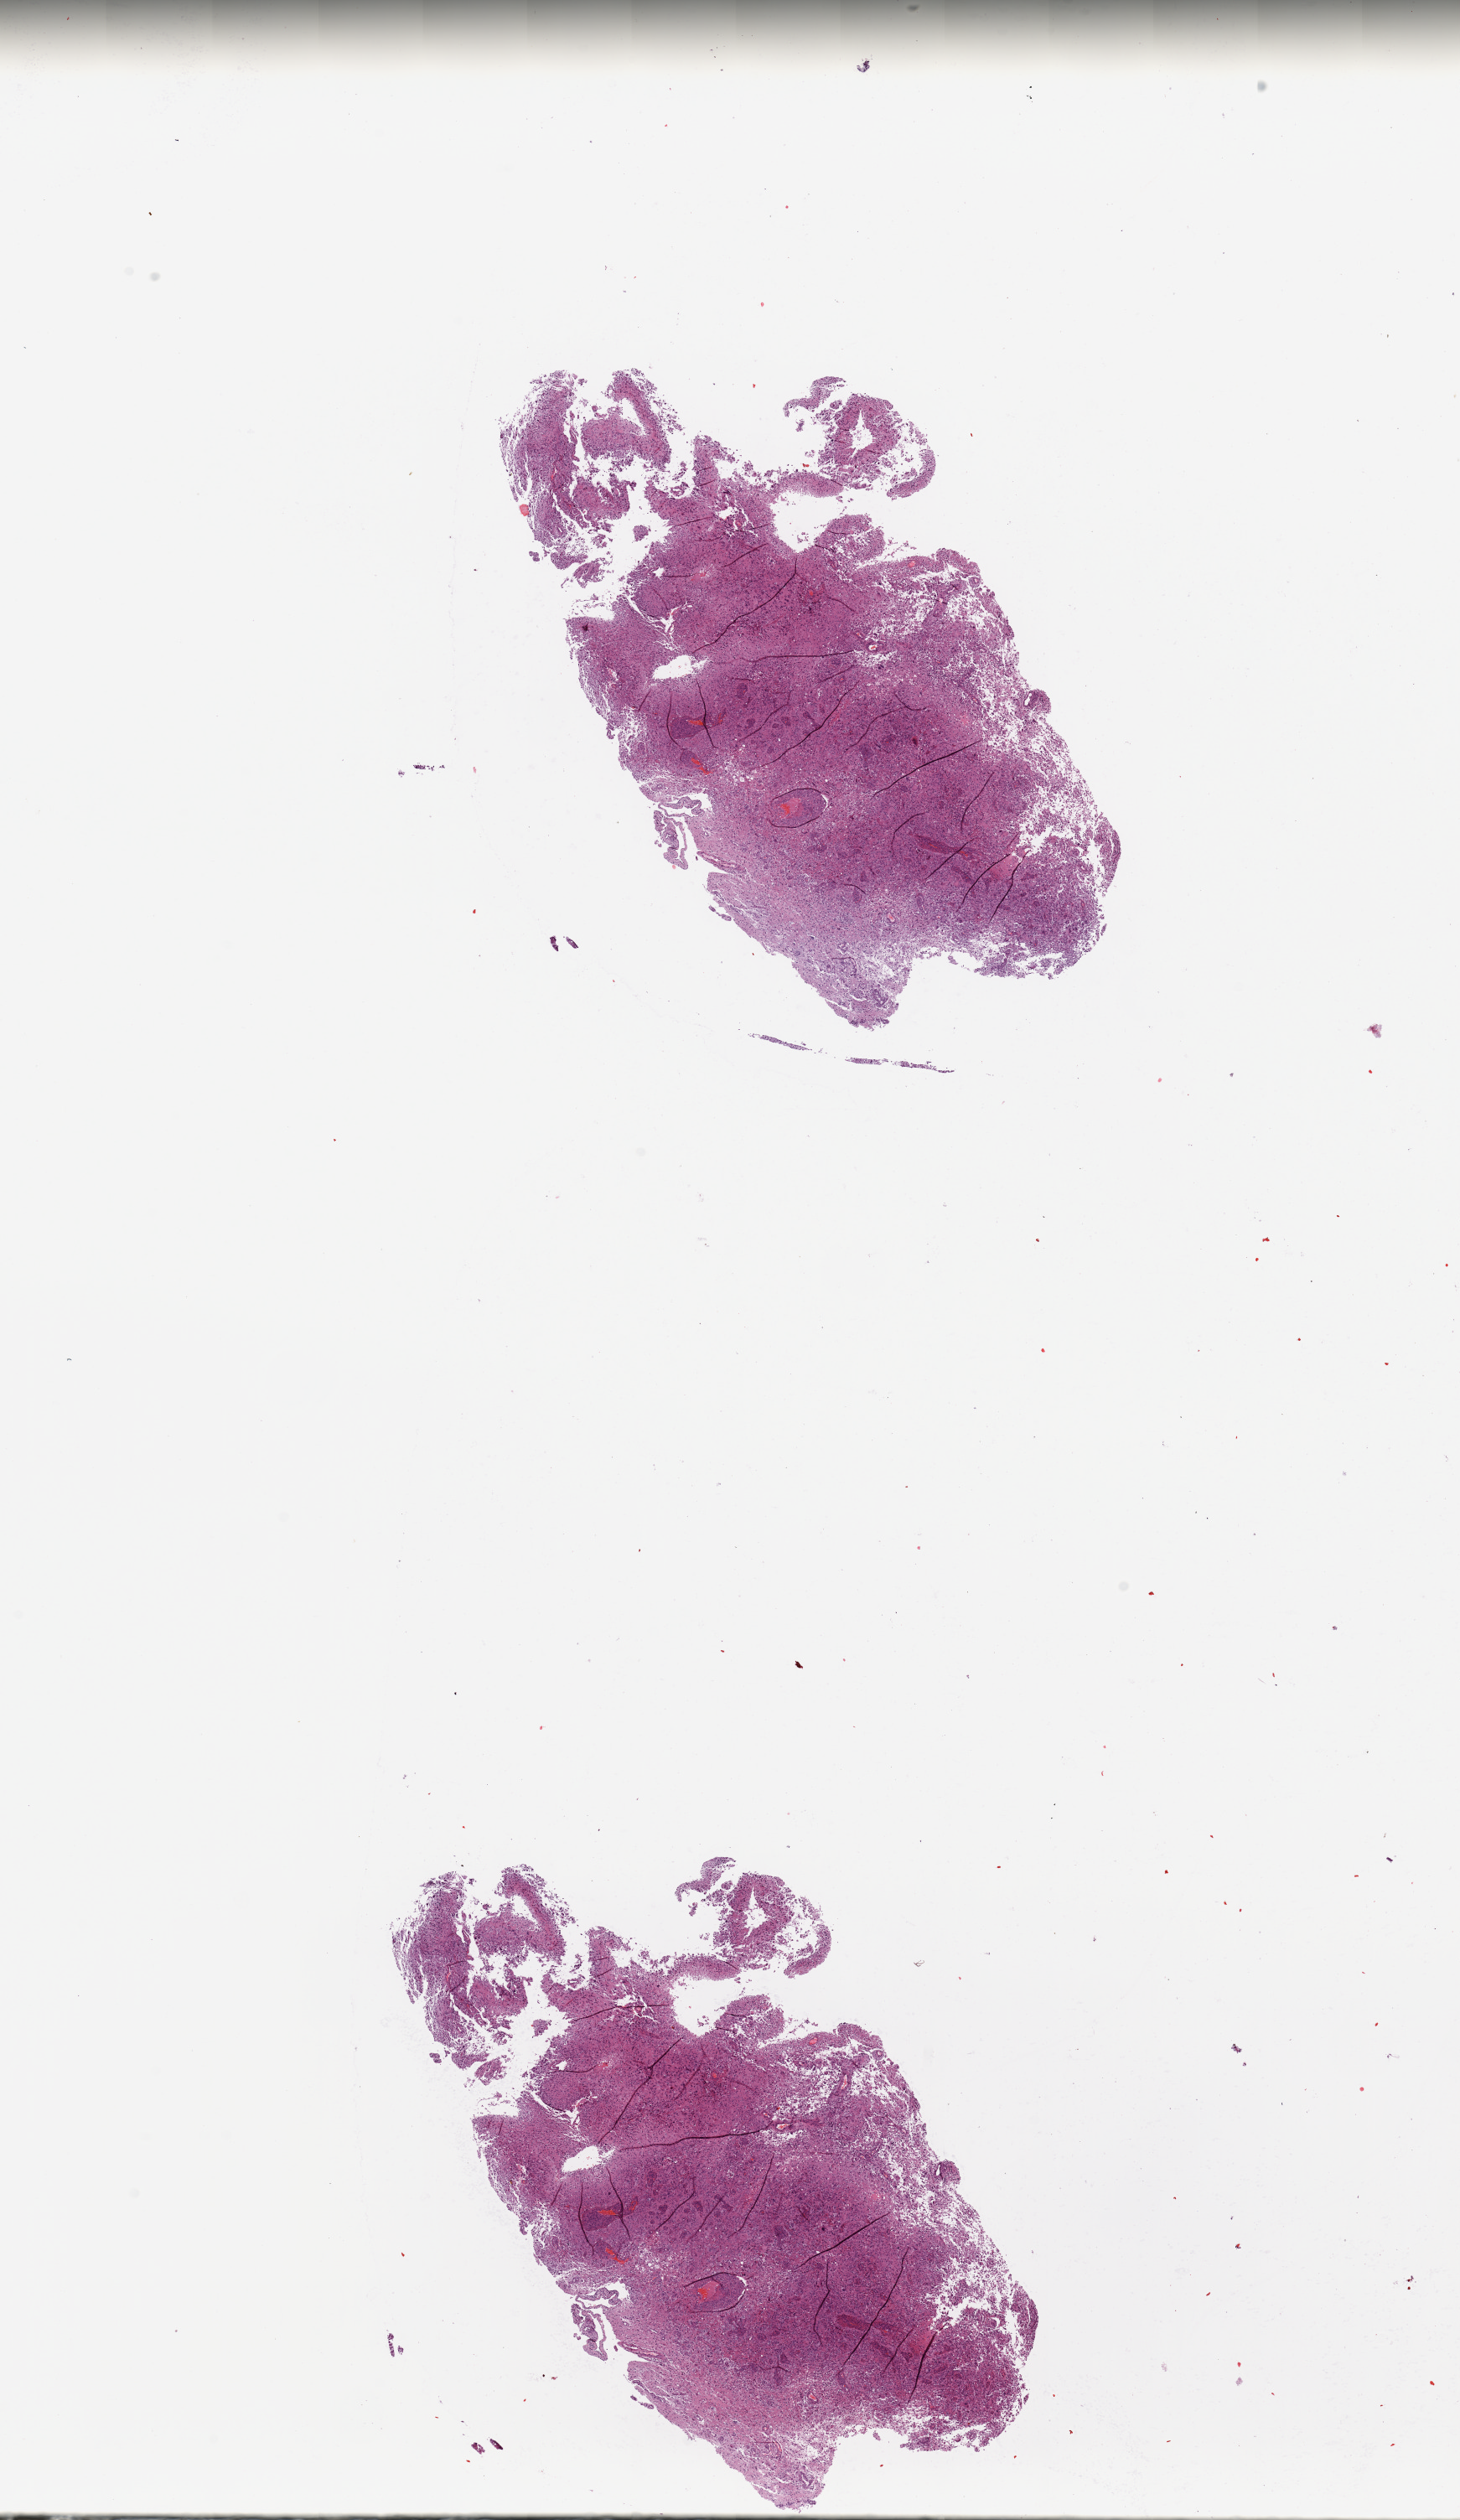
Digitized H&E tissue section (whole slide), whole scanned area (about 13.8 x 23.8 mm) shown as a low-resolution overview; tumour tissue sample, sampled site: brain. Male, 37 y/o. Slide review estimates, as recorded: tumour nuclei 80%, necrosis 20%.
Diagnosis: Glioblastoma.